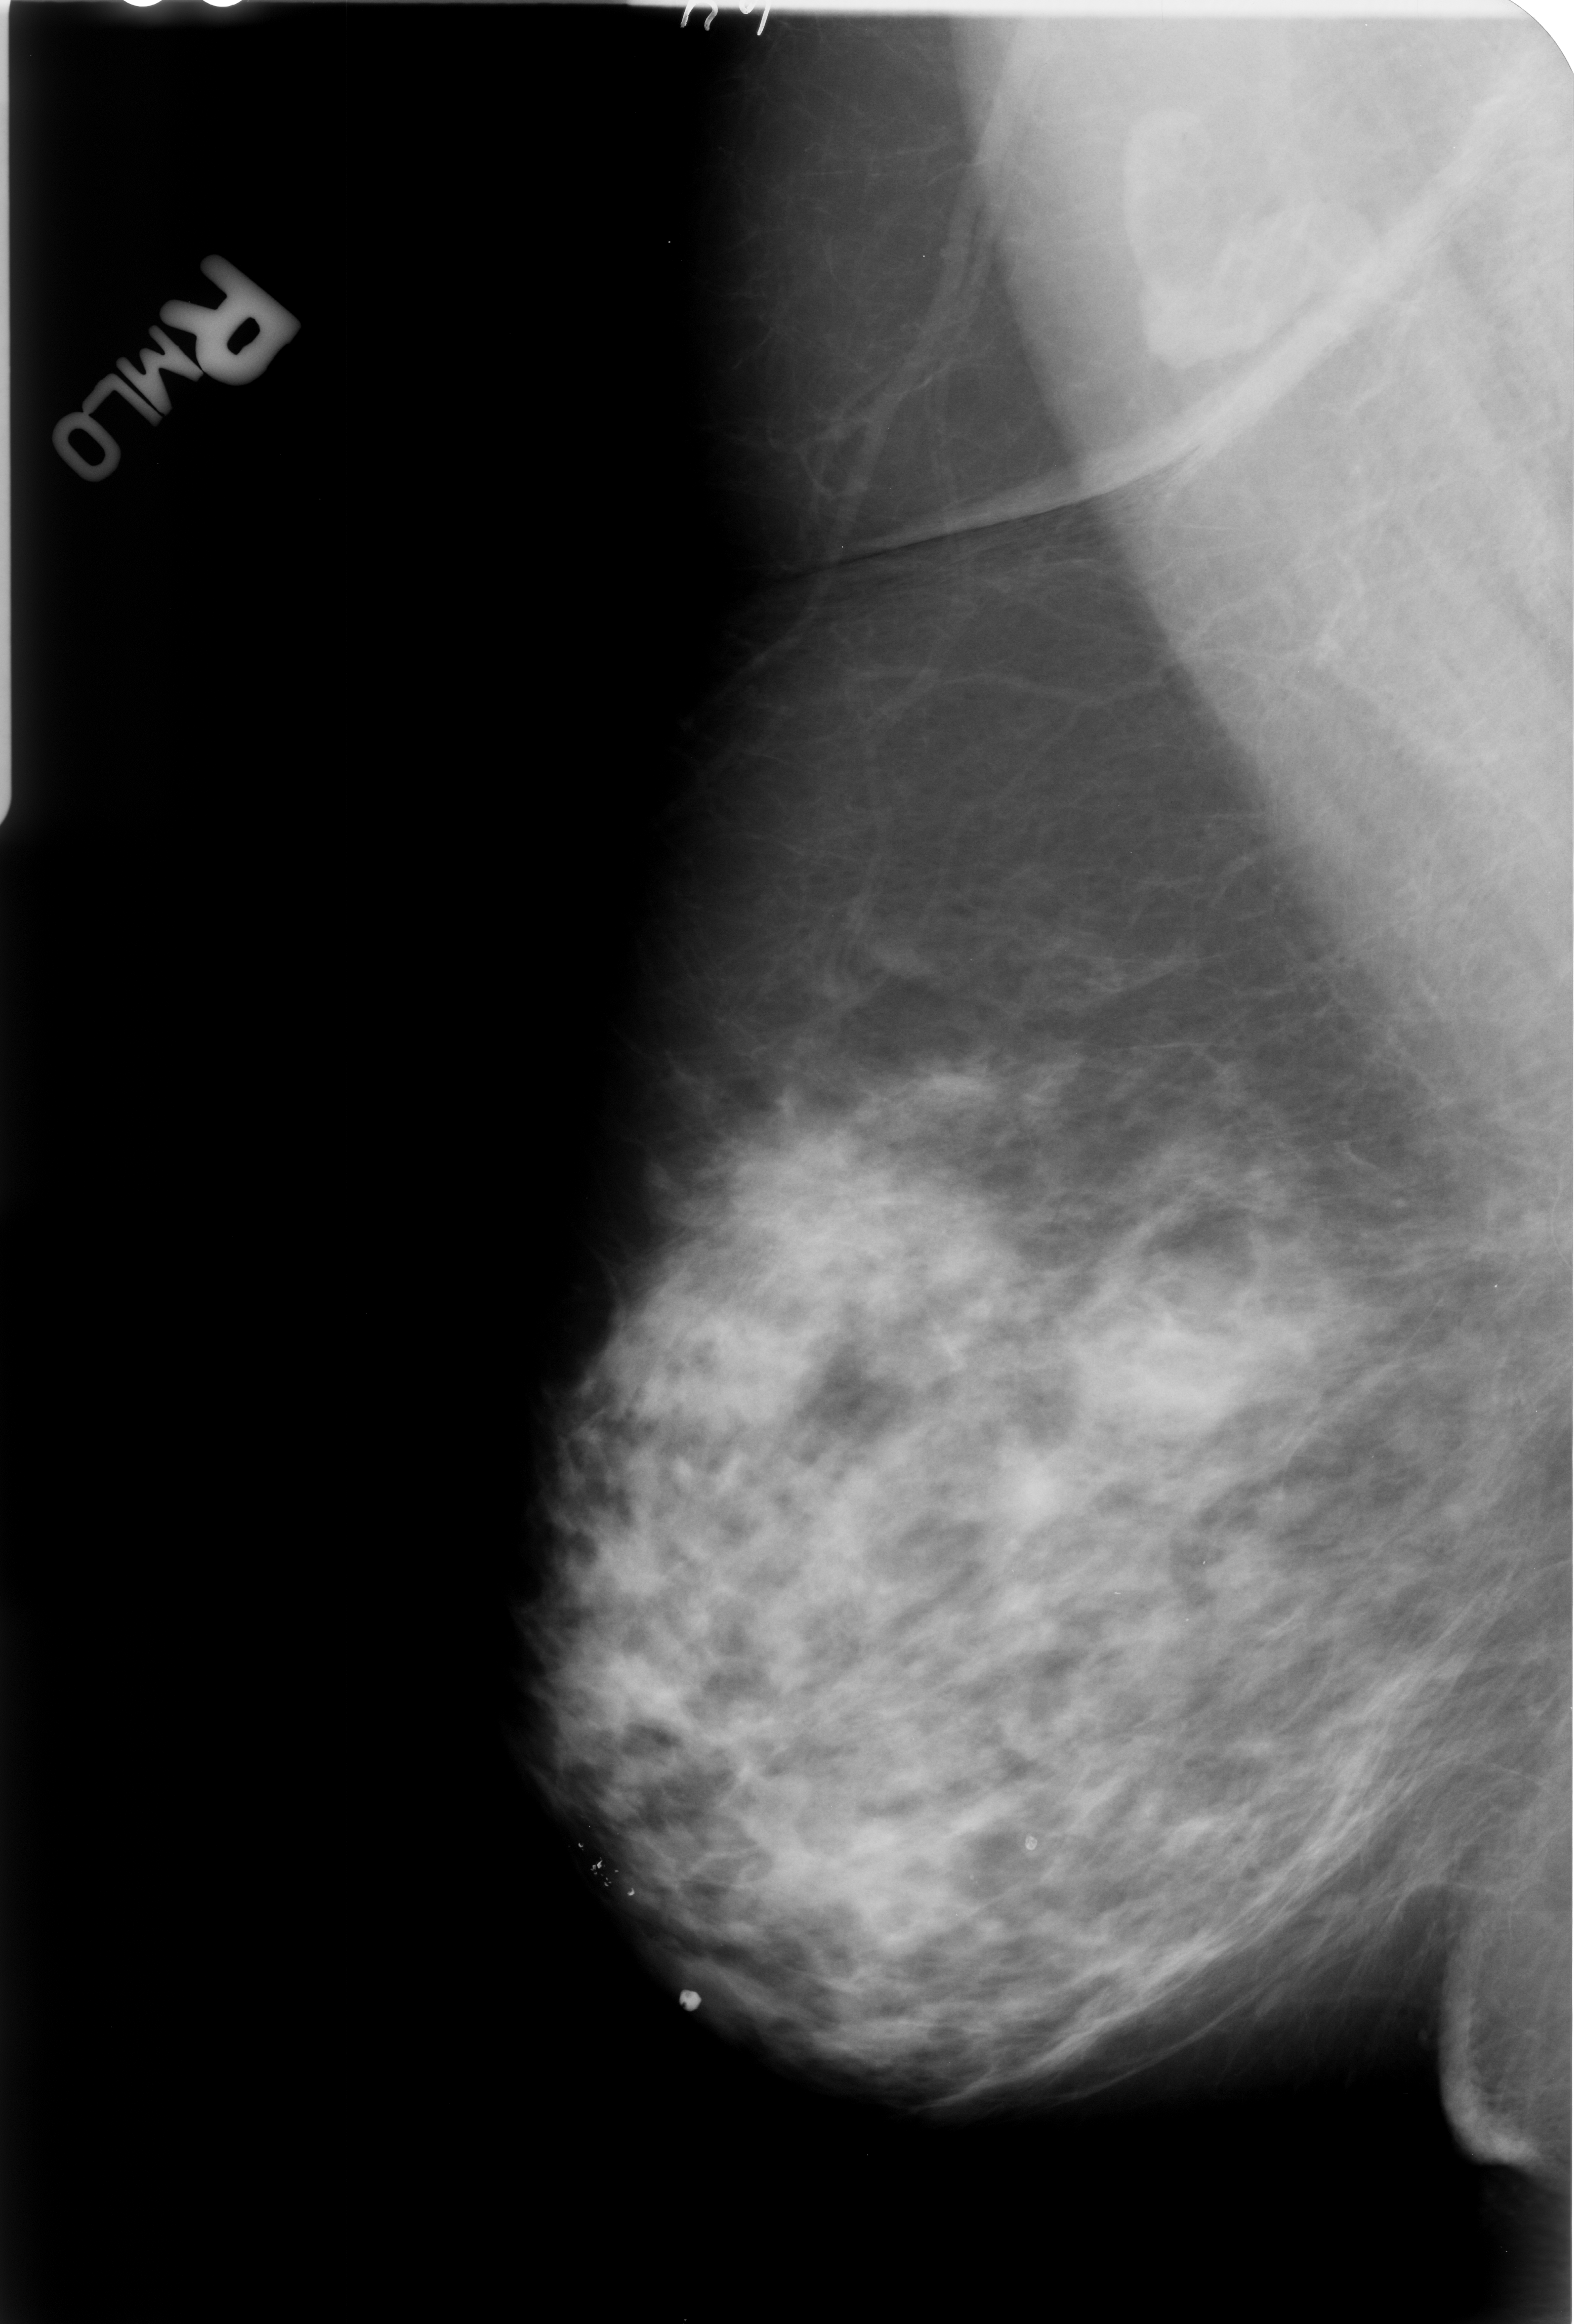
Scanned film-screen mammogram, right breast, mediolateral oblique (MLO) view, breast composition: heterogeneously dense (BI-RADS density category 3 of 4).
Radiologist-marked abnormalities on this image: Finding 1 of 2: calcifications, morphology lucent center; BI-RADS assessment category 2; benign; no additional work-up was recommended (benign without callback). Finding 2 of 2: calcifications, morphology lucent center; BI-RADS assessment category 2; benign; no additional work-up was recommended (benign without callback).